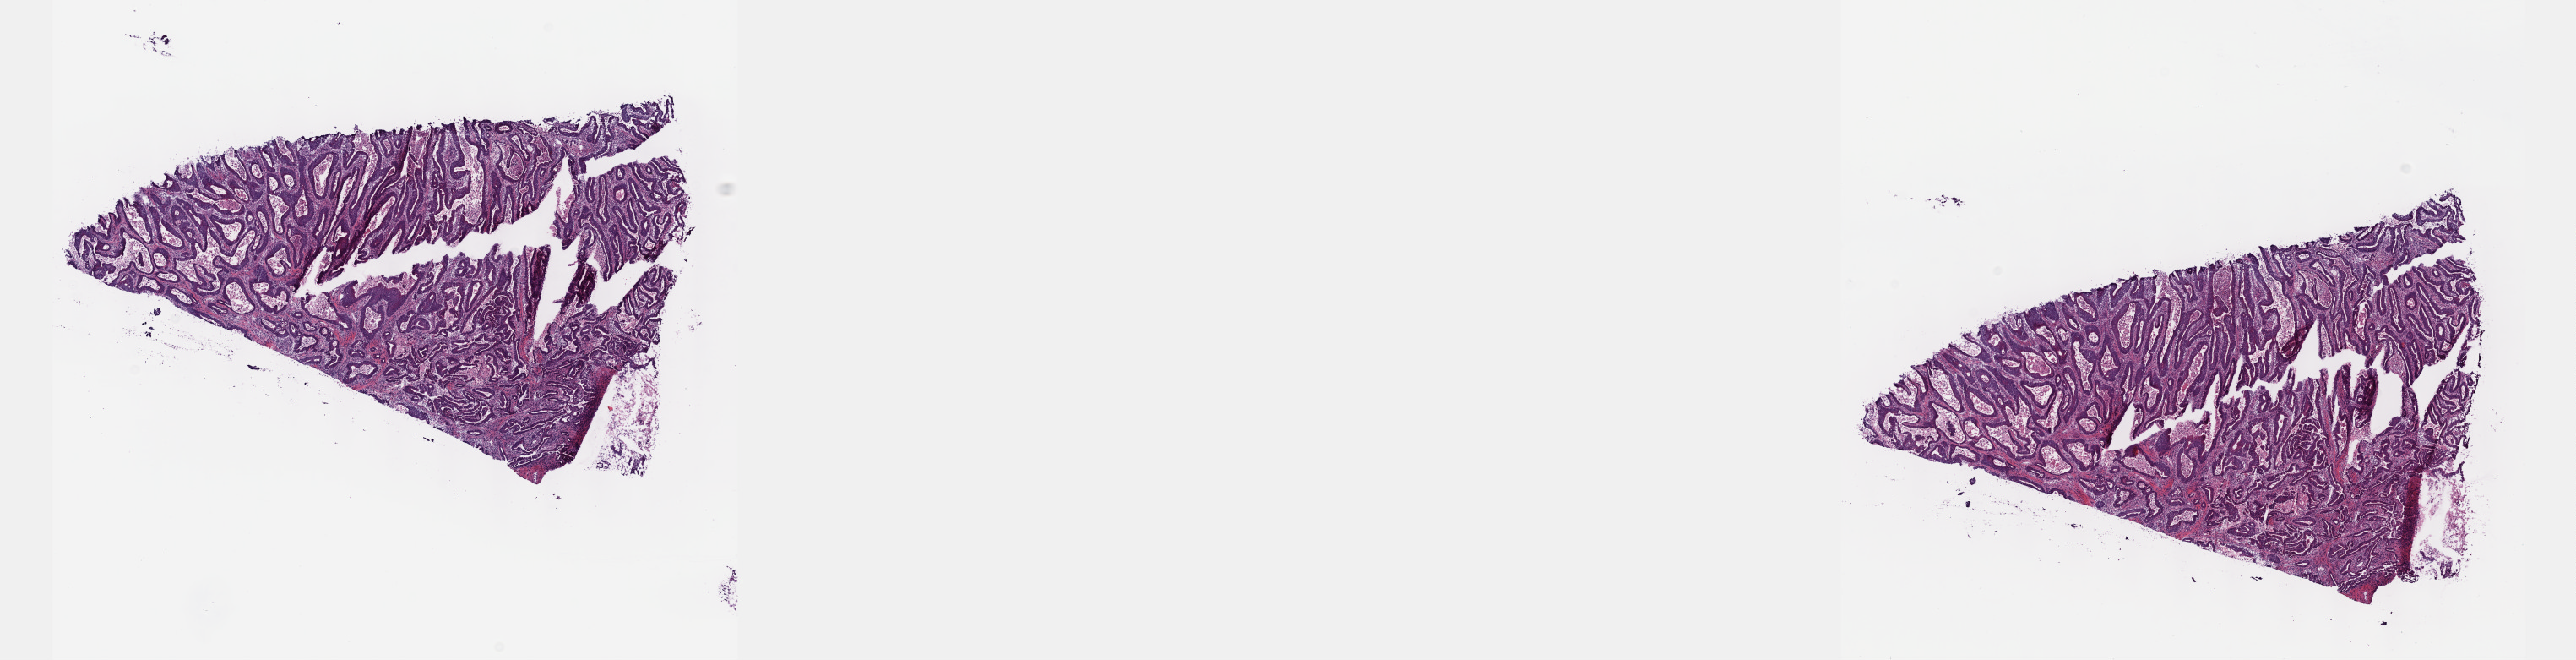
Digitized H&E tissue section (whole slide) — low-resolution overview of the scanned area, about 24.6 x 6.3 mm; frozen section from the top of the tissue portion; esophagus, primary tumour sample. Female patient; age at initial diagnosis 84 years. Pathologist review of this section (percent, as recorded): tumour cells 100%, tumour nuclei 75%.
Histologic diagnosis: Adenocarcinoma, NOS (lower third of esophagus).